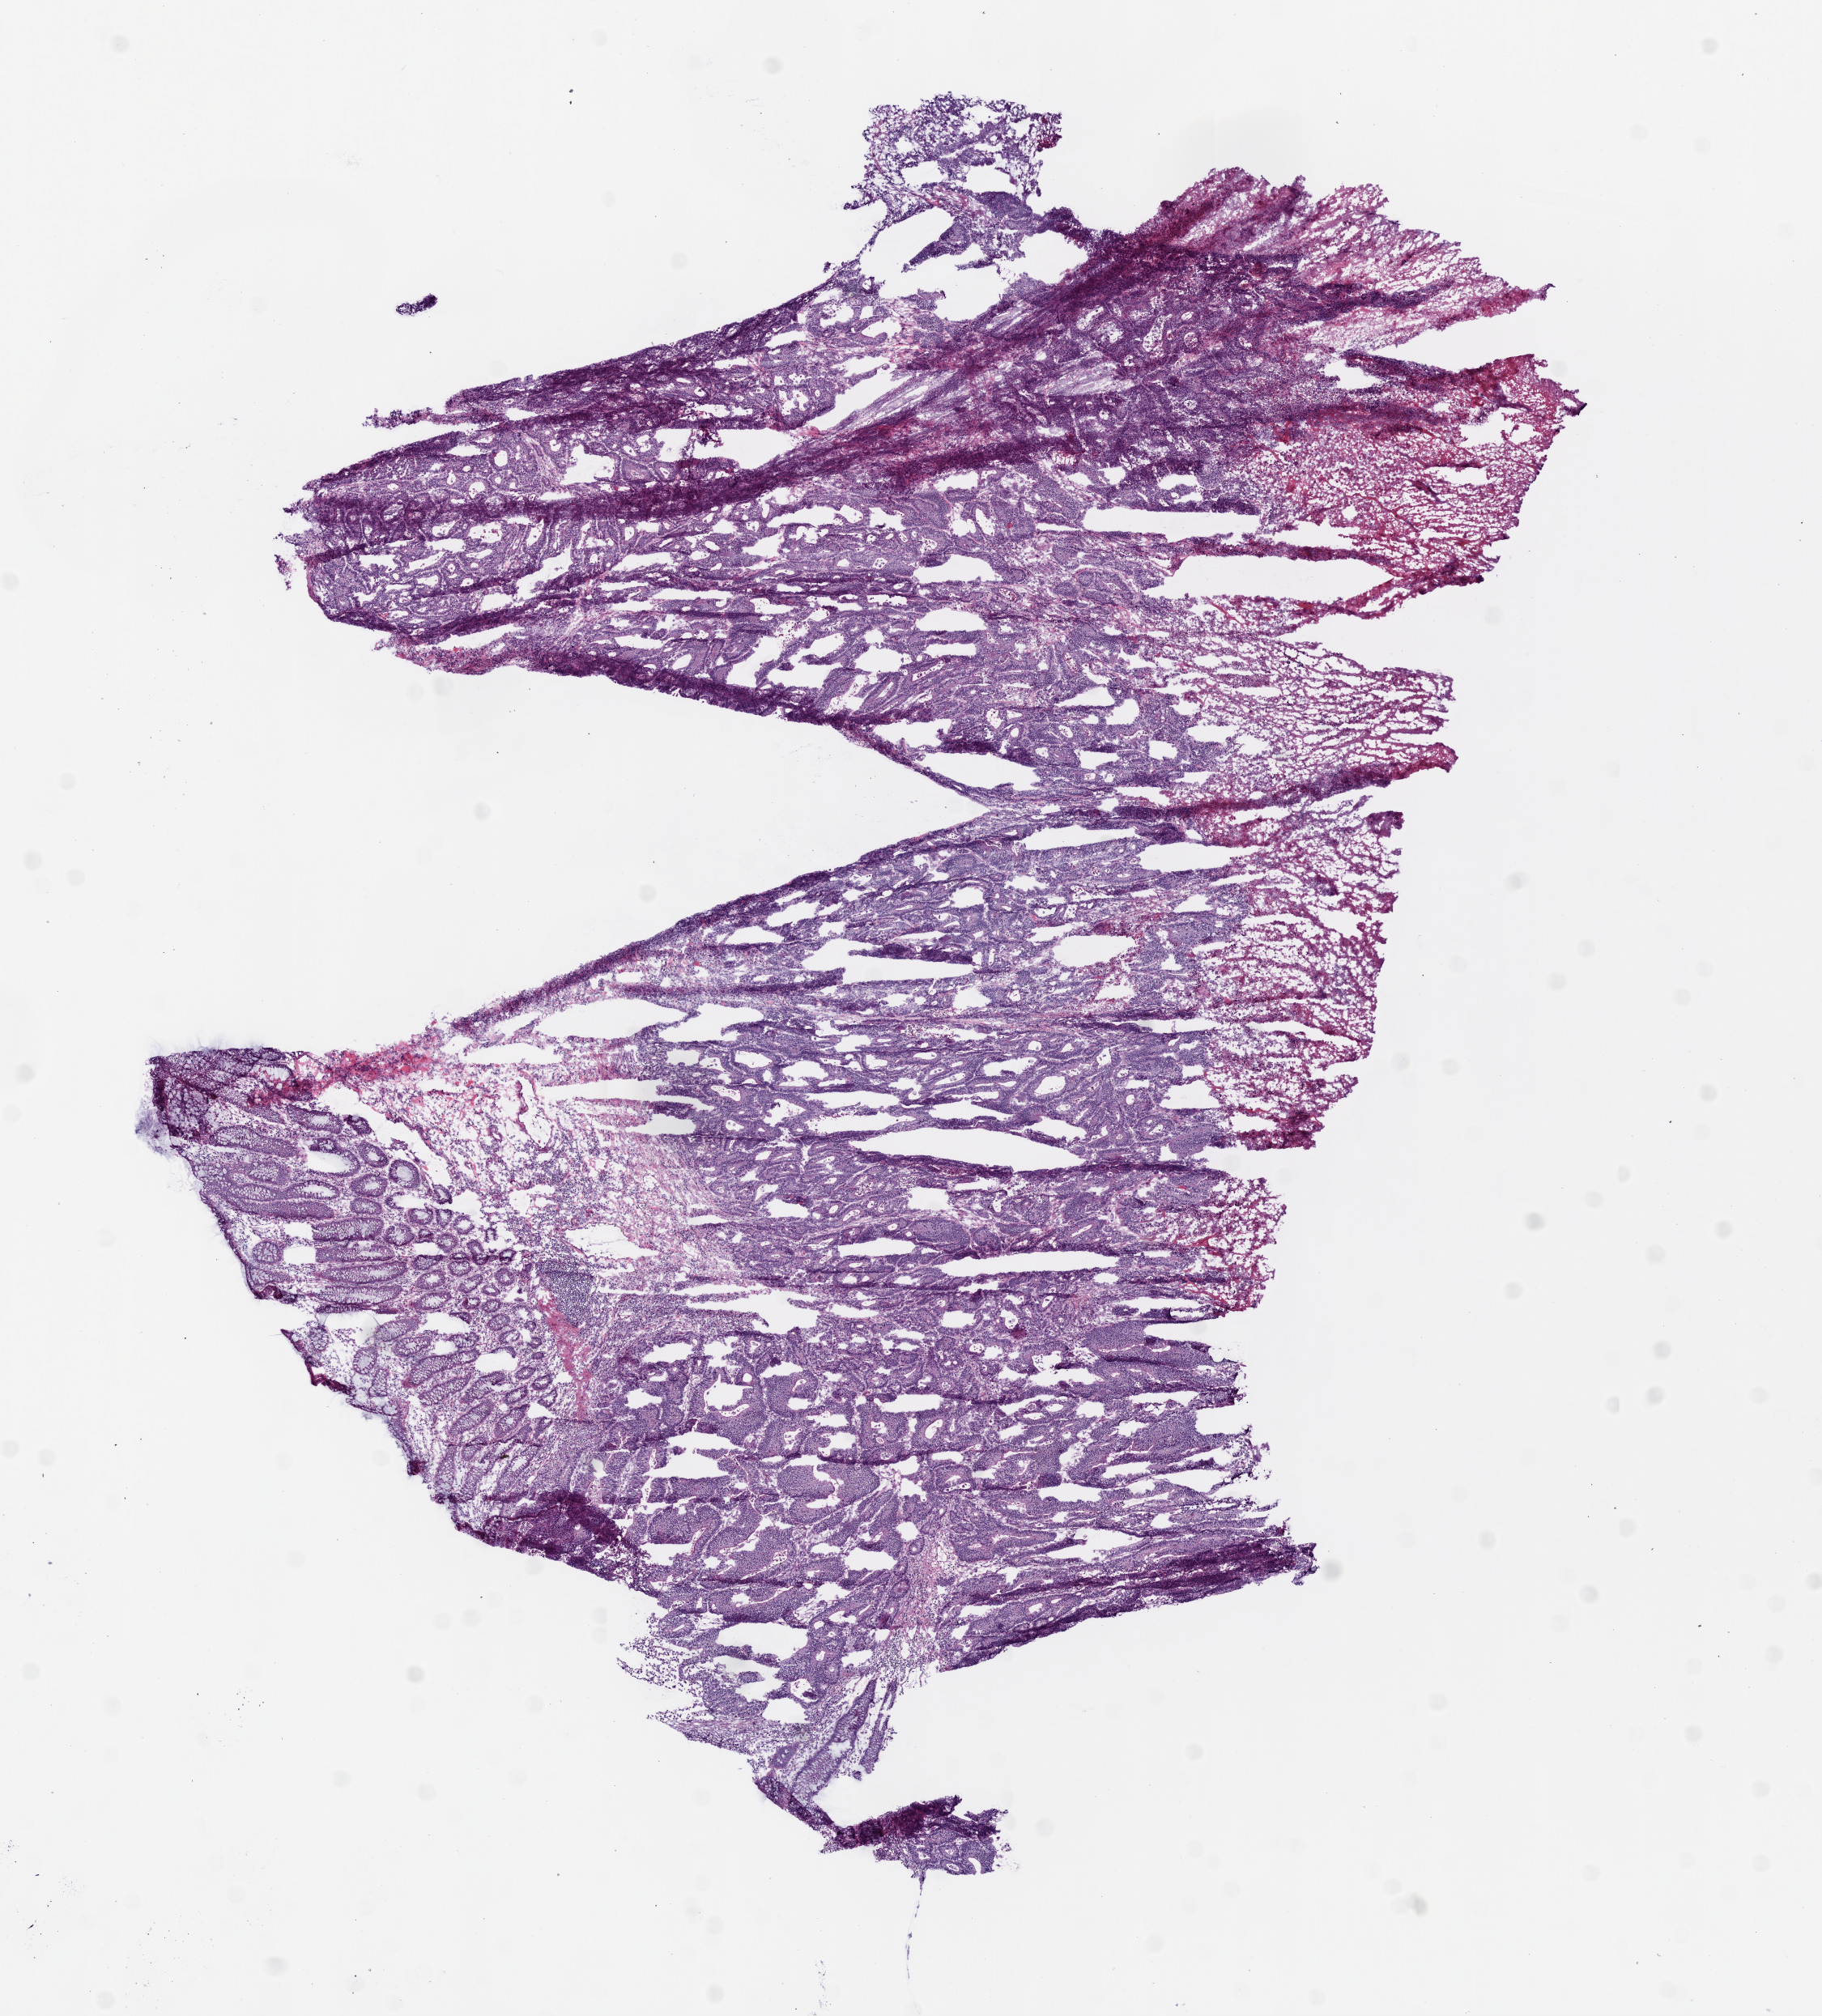
Digitized H&E-stained tissue section (whole slide), shown as a low-resolution overview of the whole scanned area (about 9.0 x 10.0 mm). Frozen section. Colon, primary tumour sample. Male, age 70 years at initial diagnosis. Pathologist review of this section (percent, as recorded): tumour cells 72%, tumour nuclei 75%, normal cells 8%, stromal cells 10%, necrosis 10%.
AJCC pathologic stage: II. Lymph nodes positive (case pathology): 0 of 44 examined. Pathologic diagnosis: Adenocarcinoma, NOS (ascending colon).